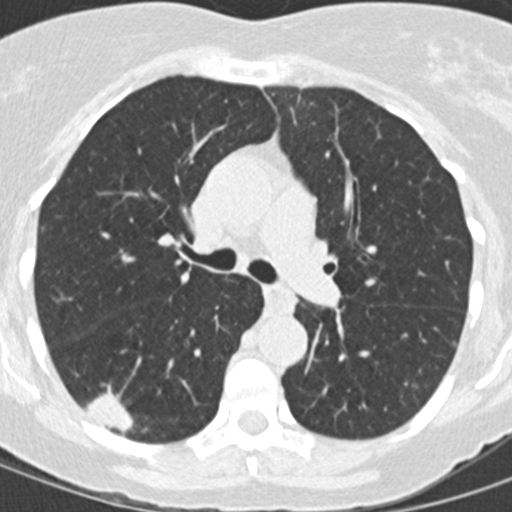
Low-dose screening chest CT, one axial slice. Position 90 of 146 along the scan axis. 120 kVp. Lung window (W 1500 / L -600 HU). 2 mm slice thickness. 512 × 512 image matrix.
Structures marked on this image (expert manual segmentation):
- lesion 1 (tumor, lower lobe of right lung): bounding box [x1, y1, x2, y2] px = [86, 391, 134, 433]